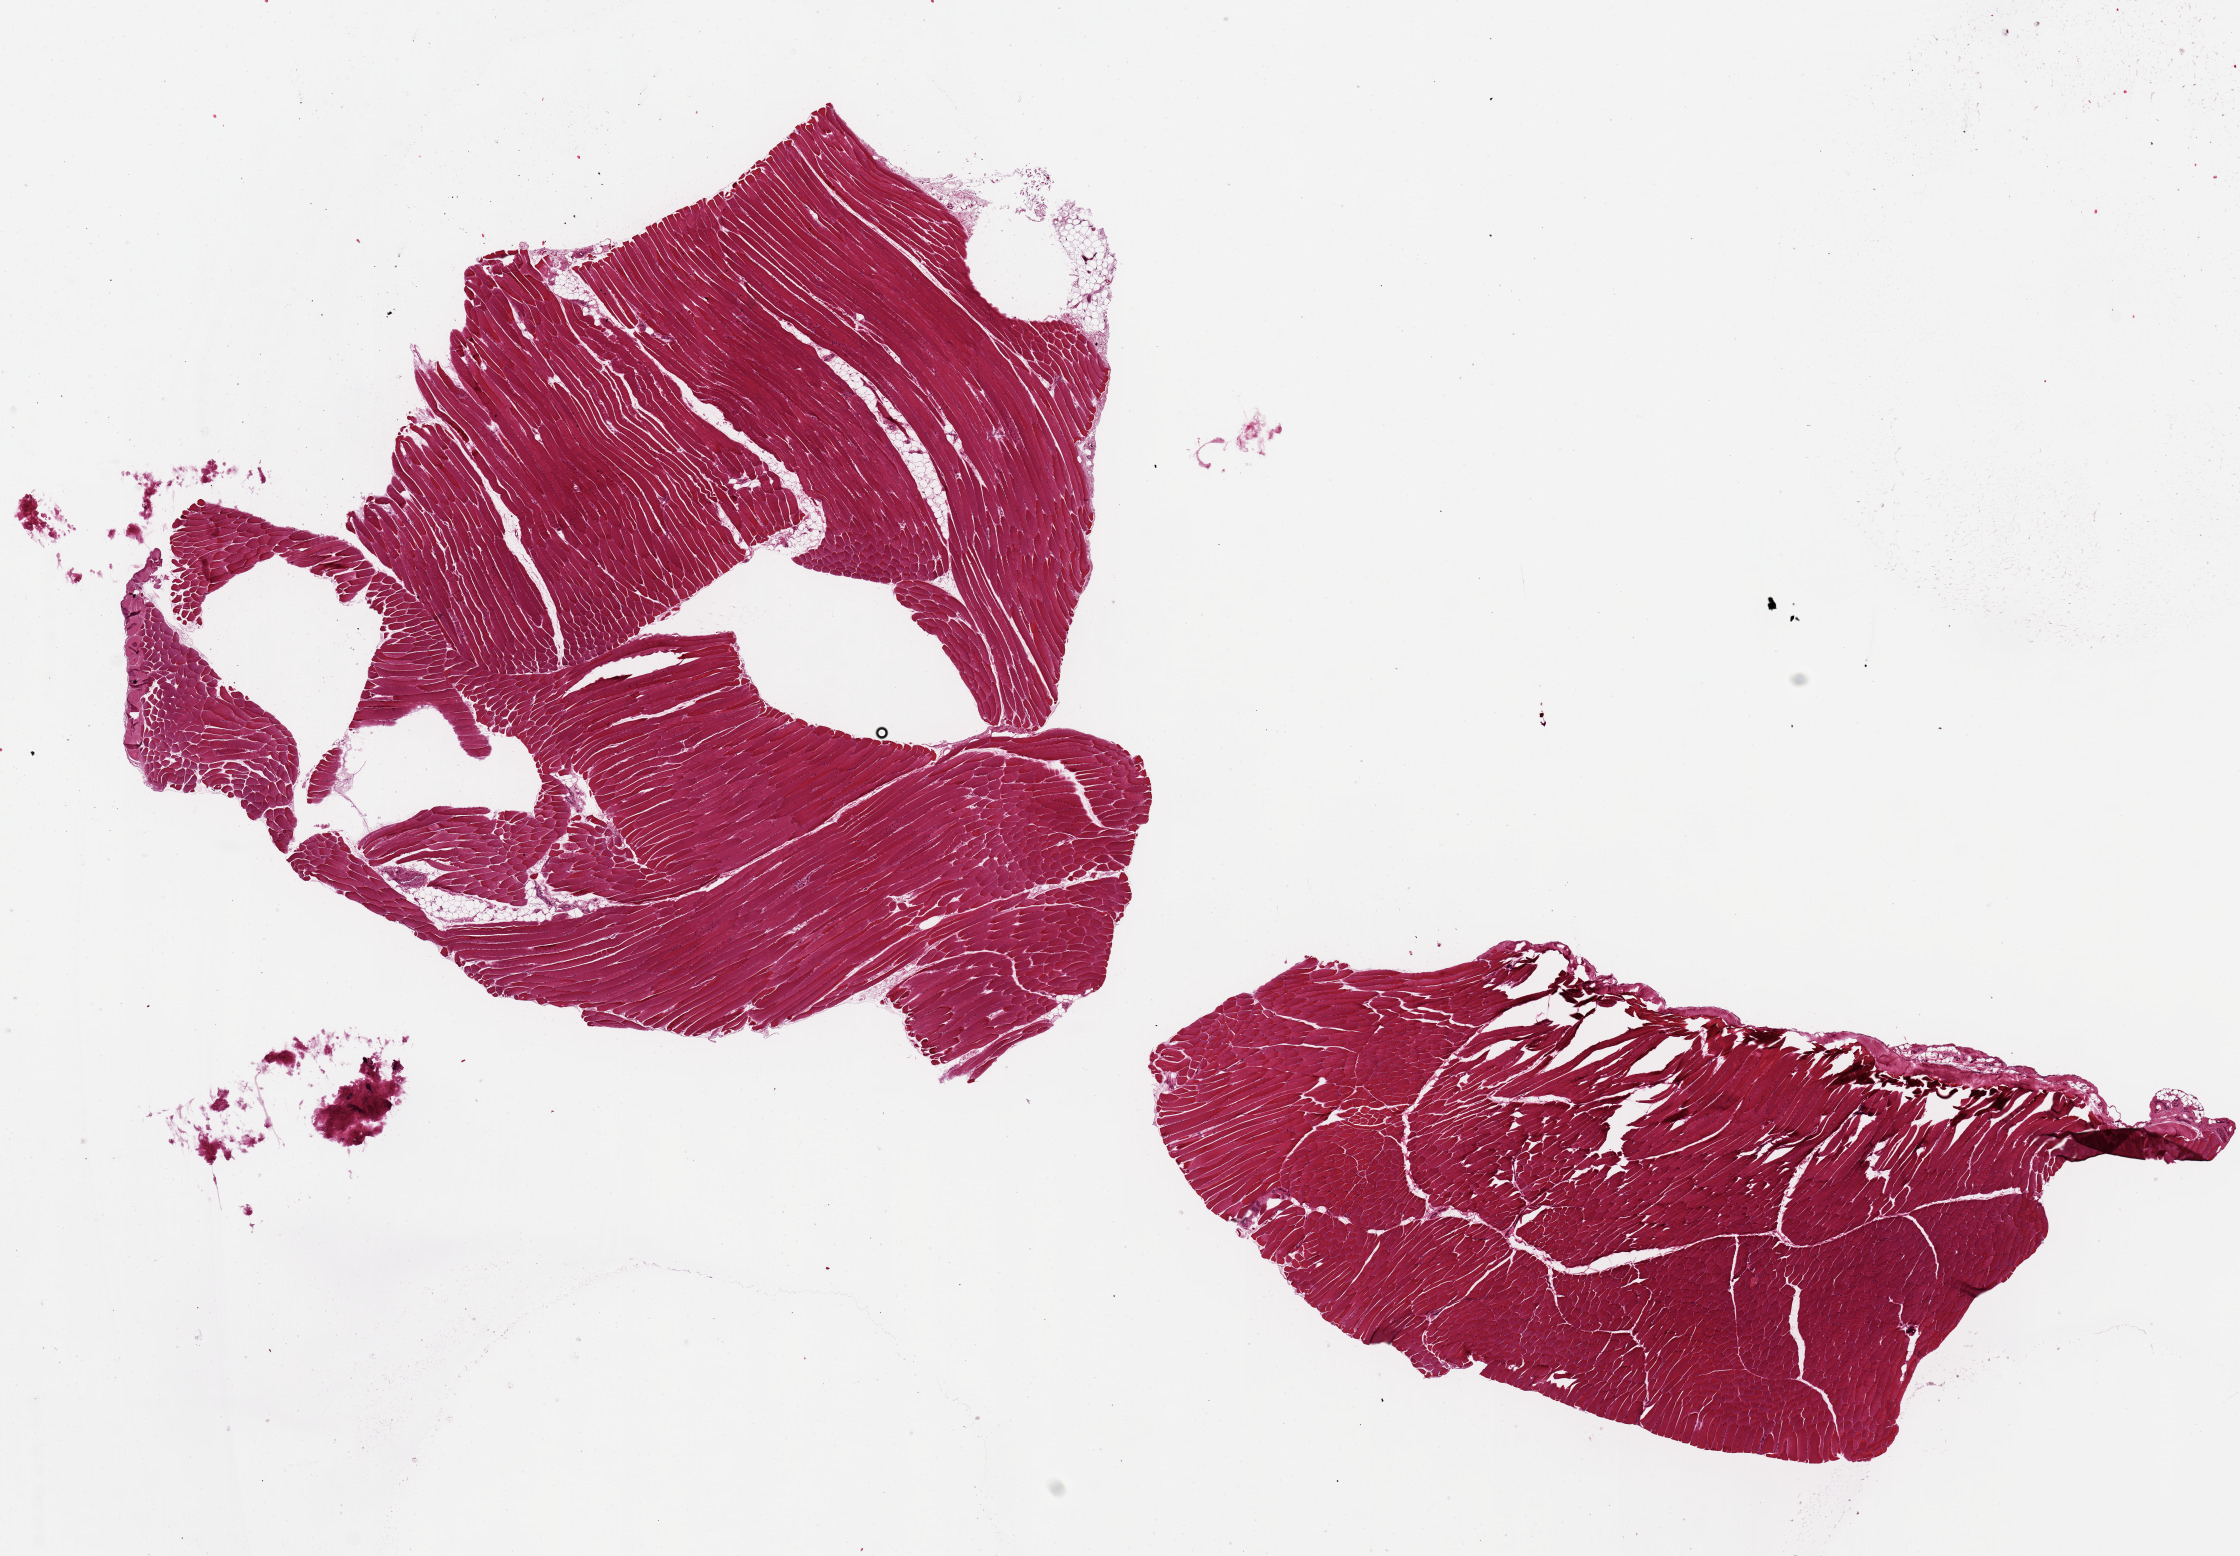
Whole-slide image, hematoxylin and eosin (H&E) stain, a low-resolution overview of the entire scanned area, about 17.7 x 12.3 mm (slide scanned at 20x); PAXgene-fixed, paraffin-embedded tissue; target tissue: skeletal muscle; donor tissue sample.
Reviewer comment on this tissue sample: 2 pieces~7x5mm, minimal fat.